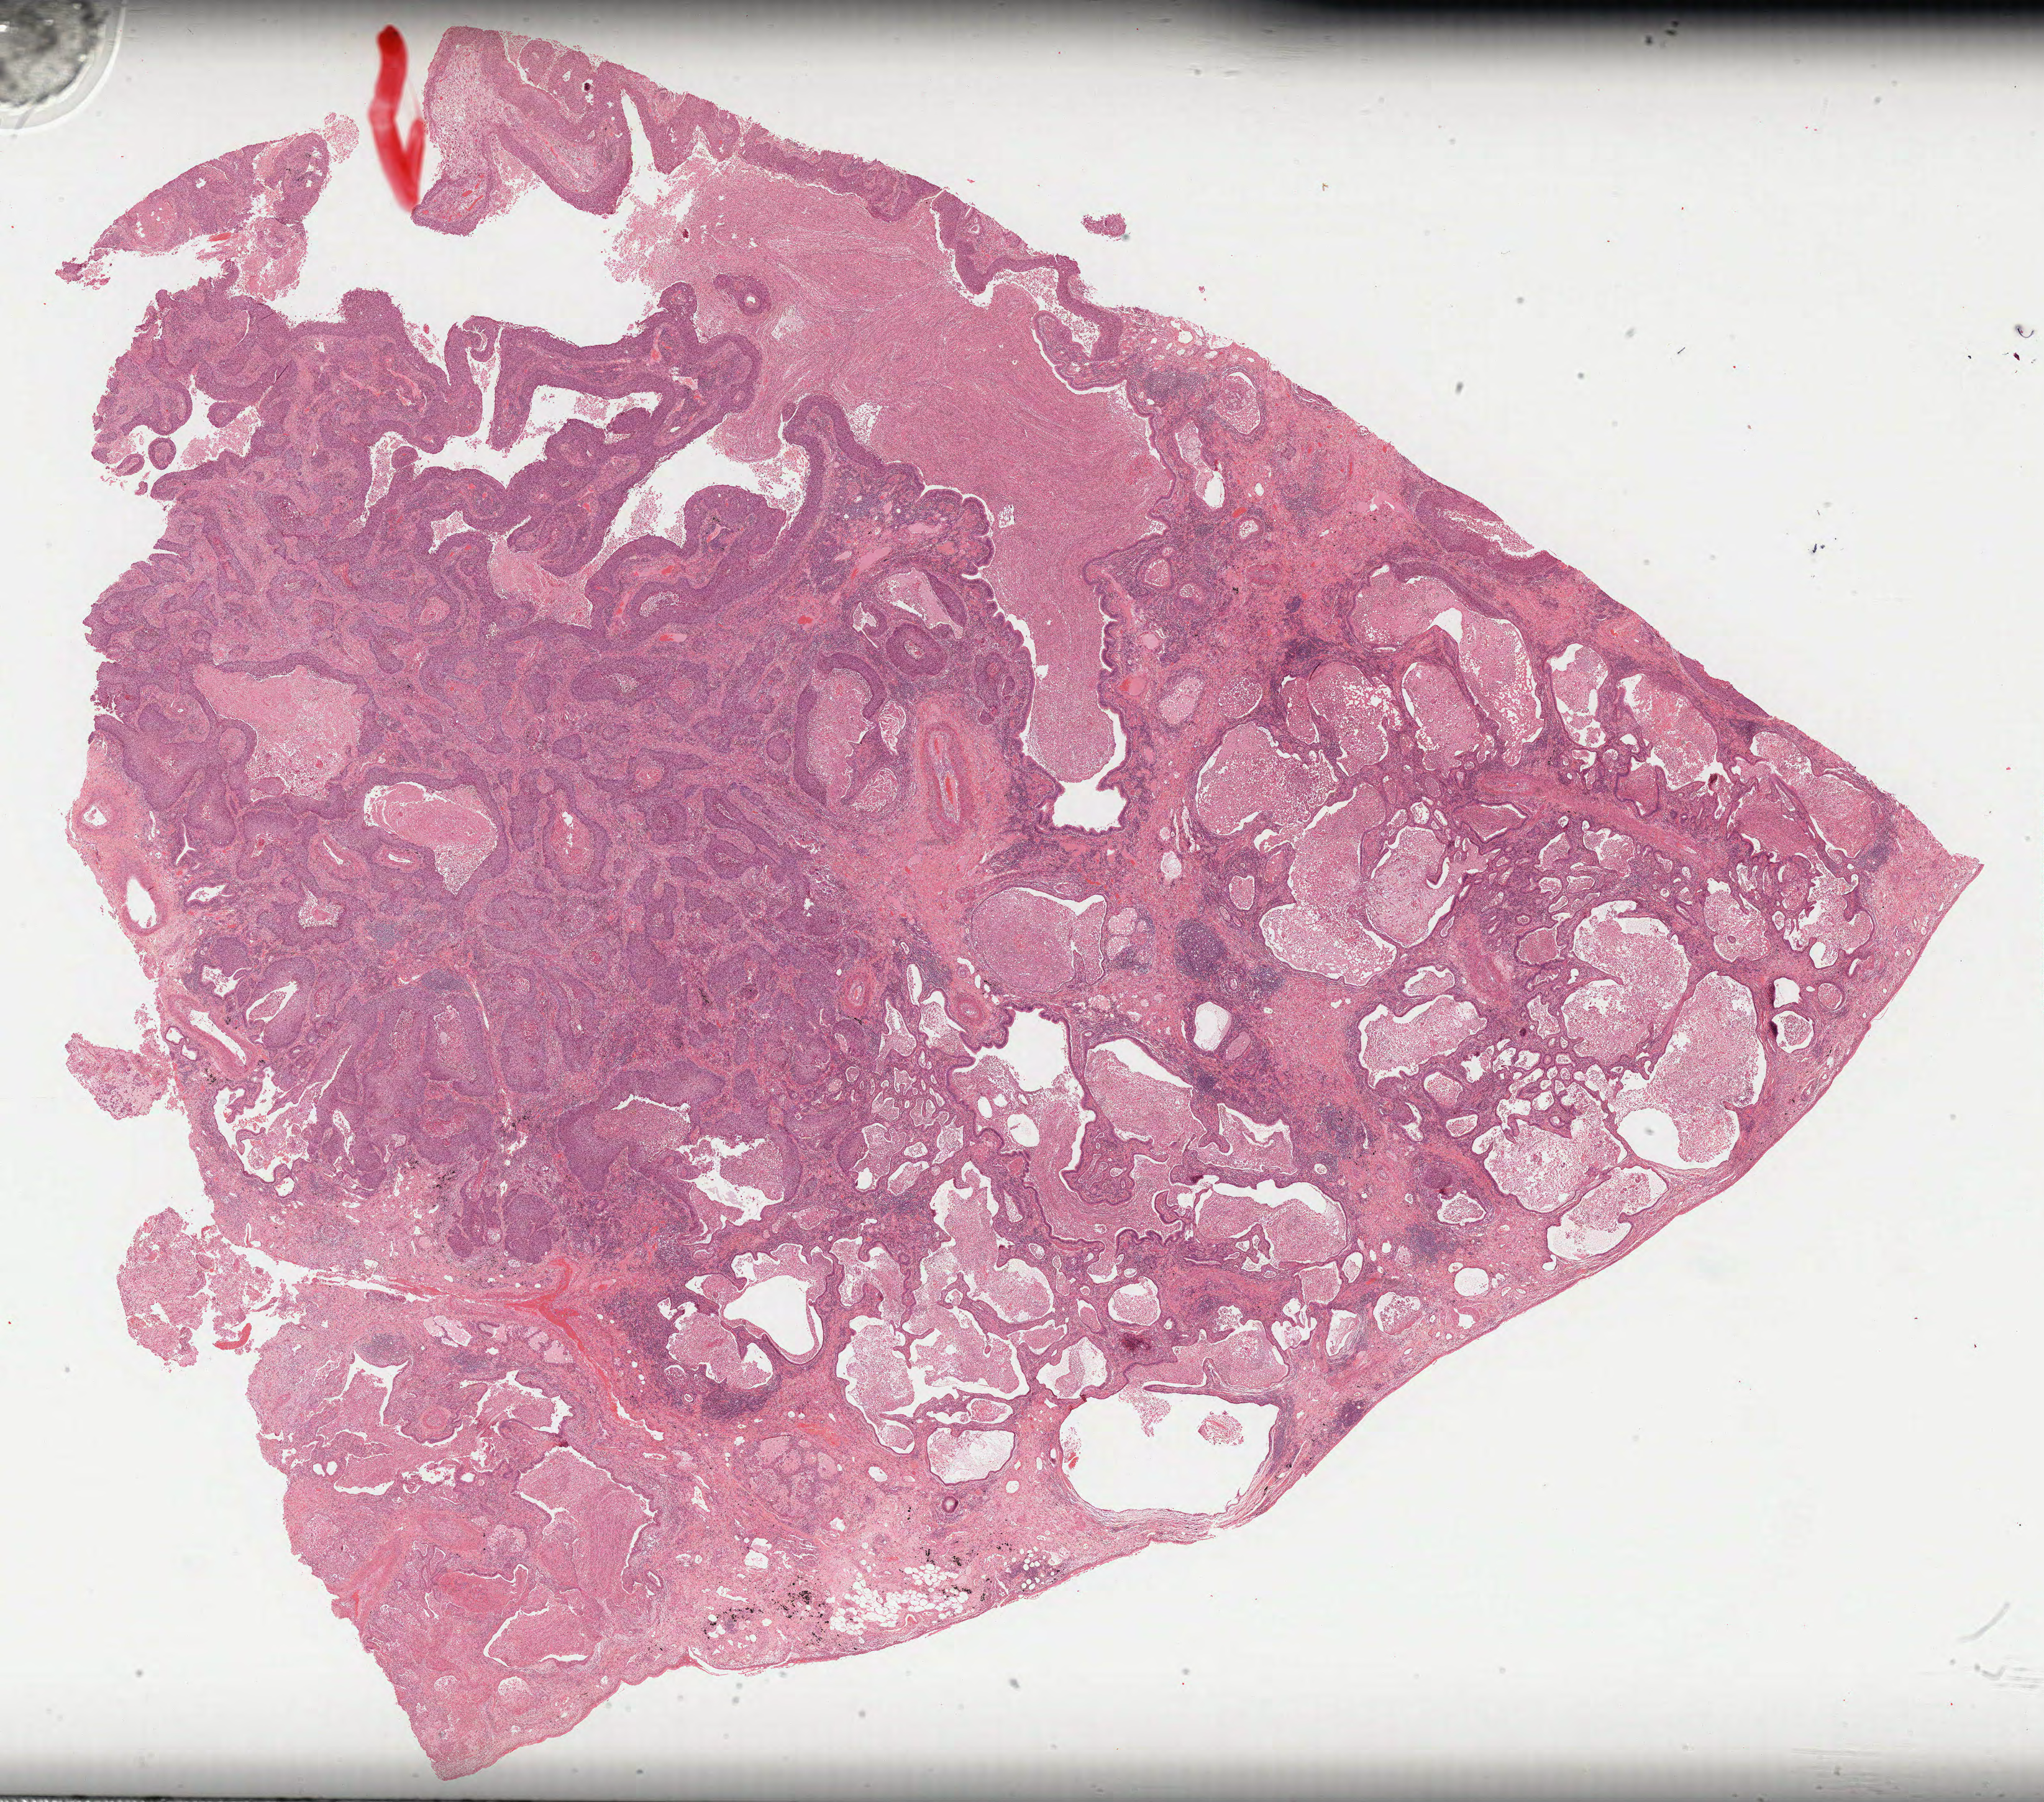
H&E-stained whole-slide image, whole scanned area (about 26.5 x 23.4 mm, acquisition: 40x scan) shown as a low-resolution overview. Formalin-fixed paraffin-embedded (FFPE) diagnostic section. Lung, primary tumour sample. Patient: male, age at initial diagnosis 64 years.
Diagnosis: Squamous cell carcinoma, NOS (lower lobe, lung). Laterality: right. AJCC pathologic stage: IB.